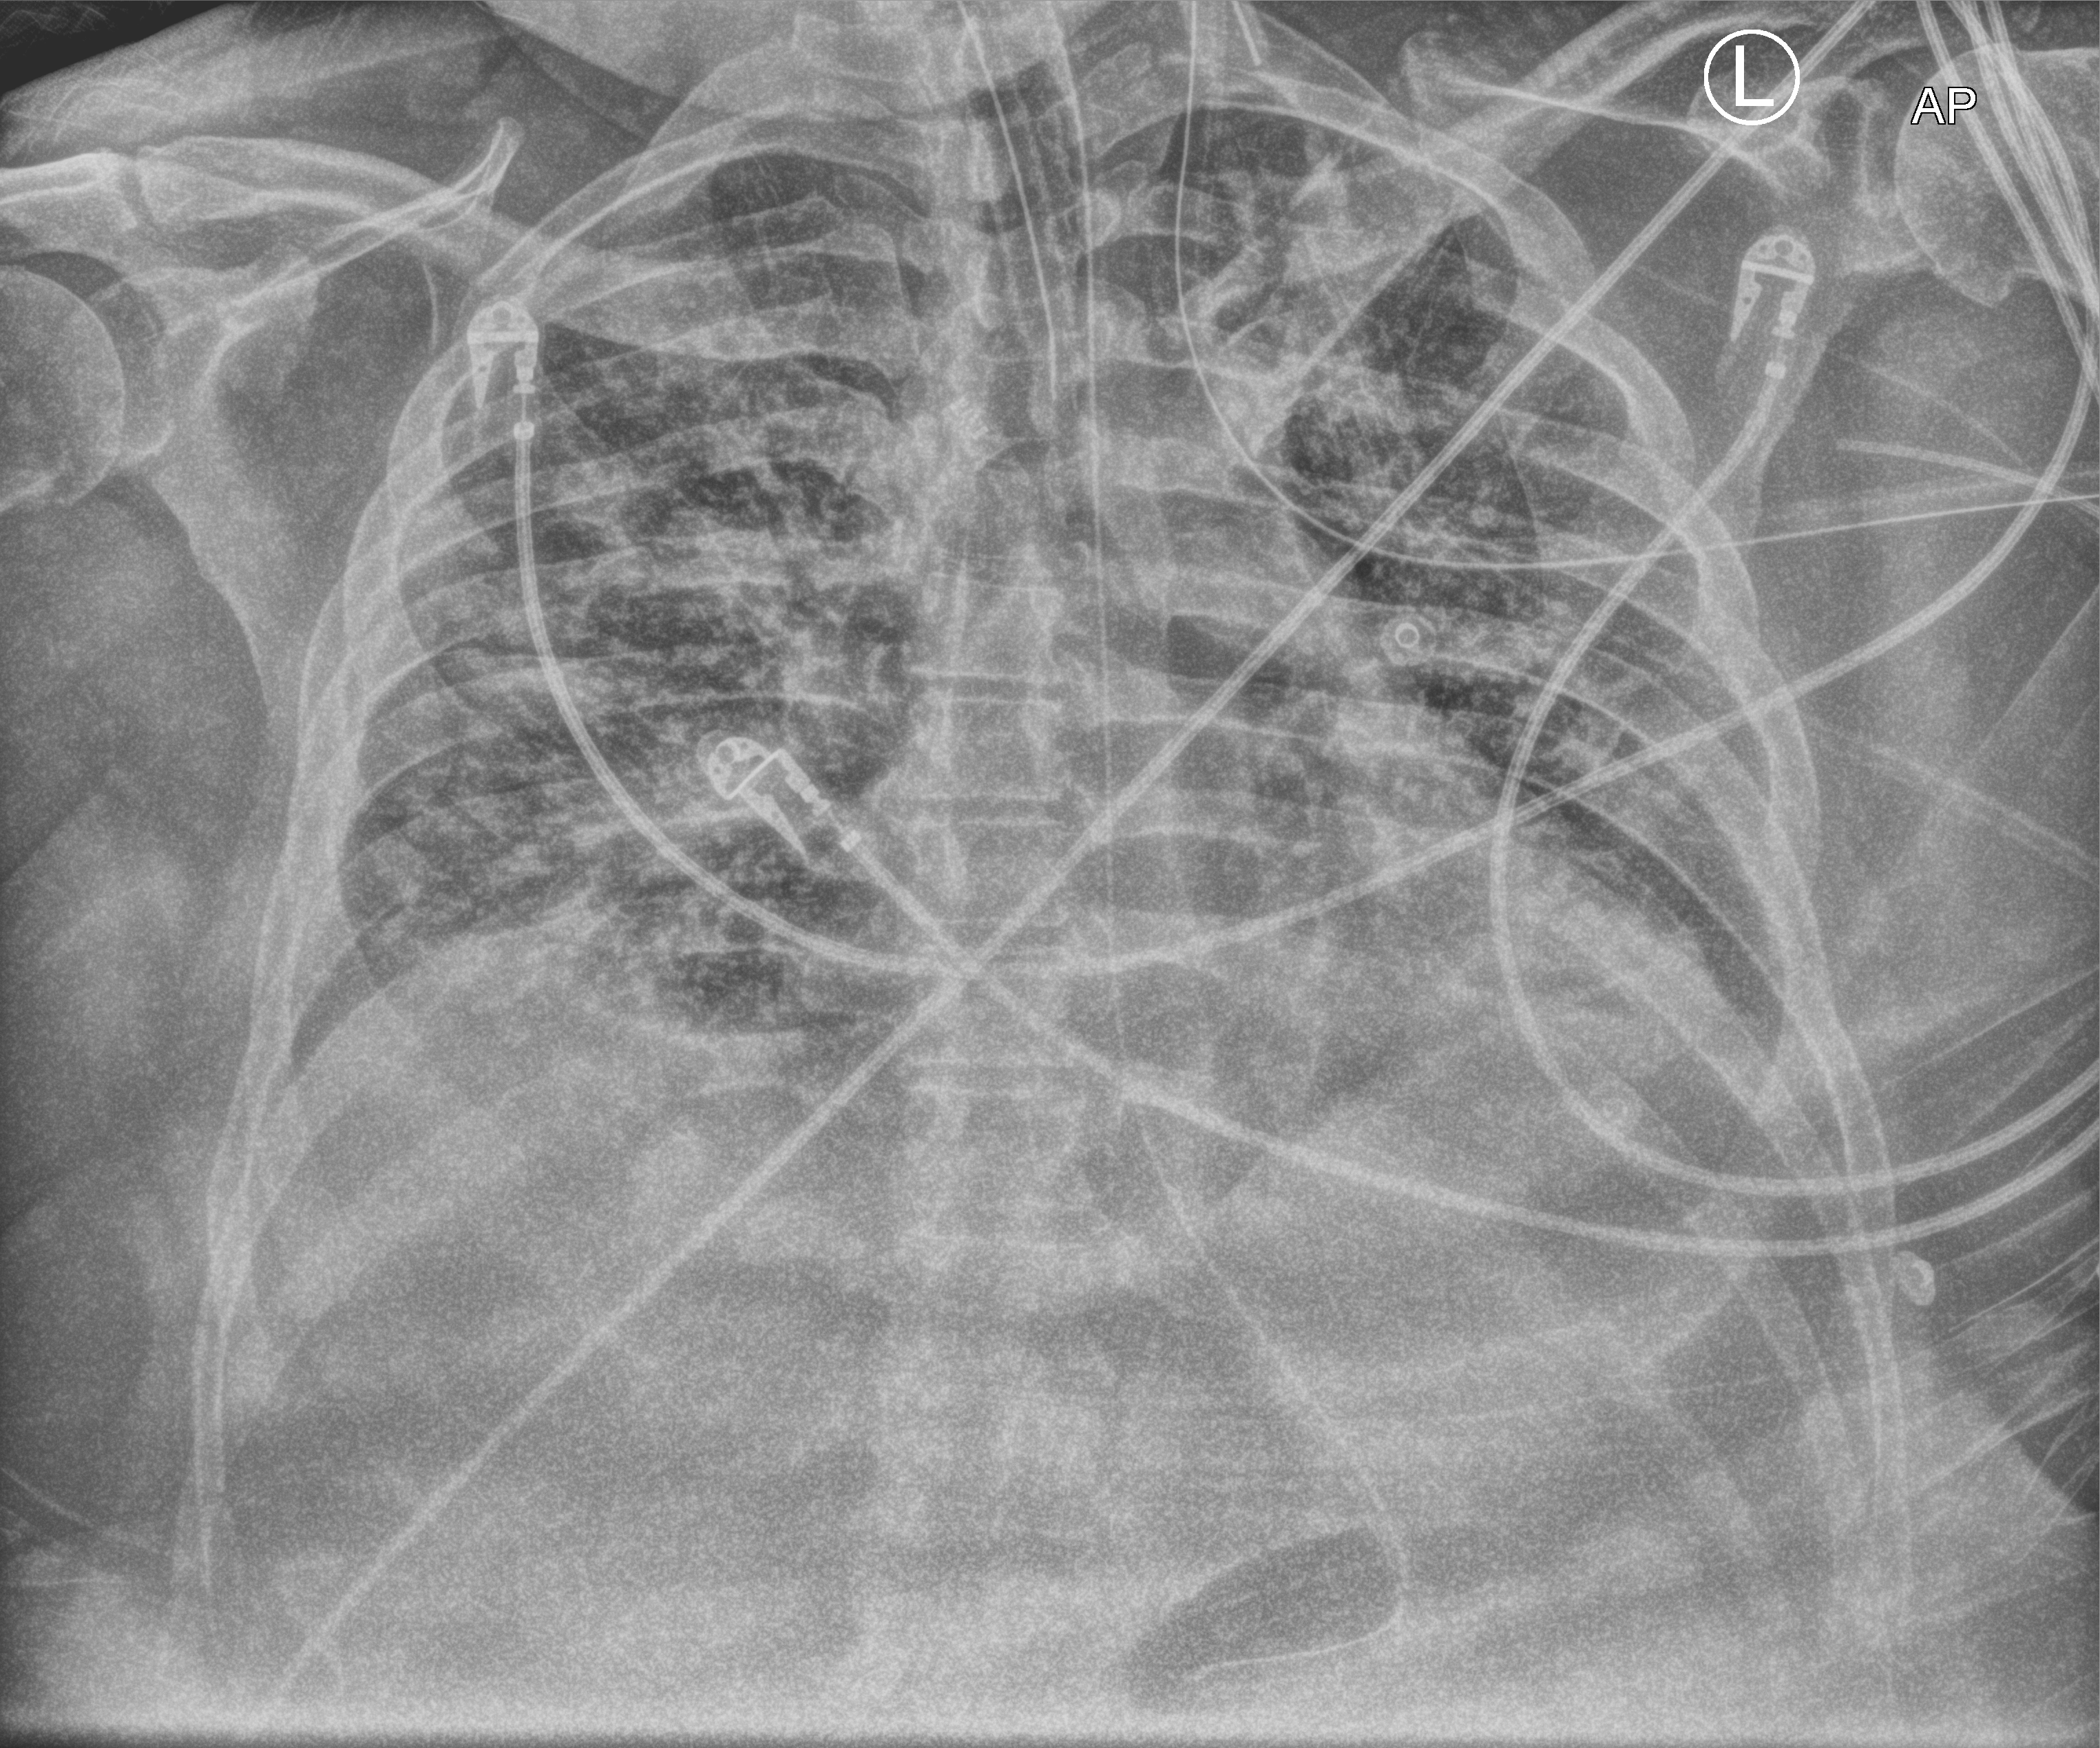
Portable chest radiograph. Male patient hospitalised with COVID-19, age 18–59 years.
From the hospital-stay record, not from the radiograph (when in the stay this image was taken is not recorded):
- mechanically ventilated during this hospital stay: yes
- admitted to intensive care during this hospital stay: yes
- COPD (admission record): no